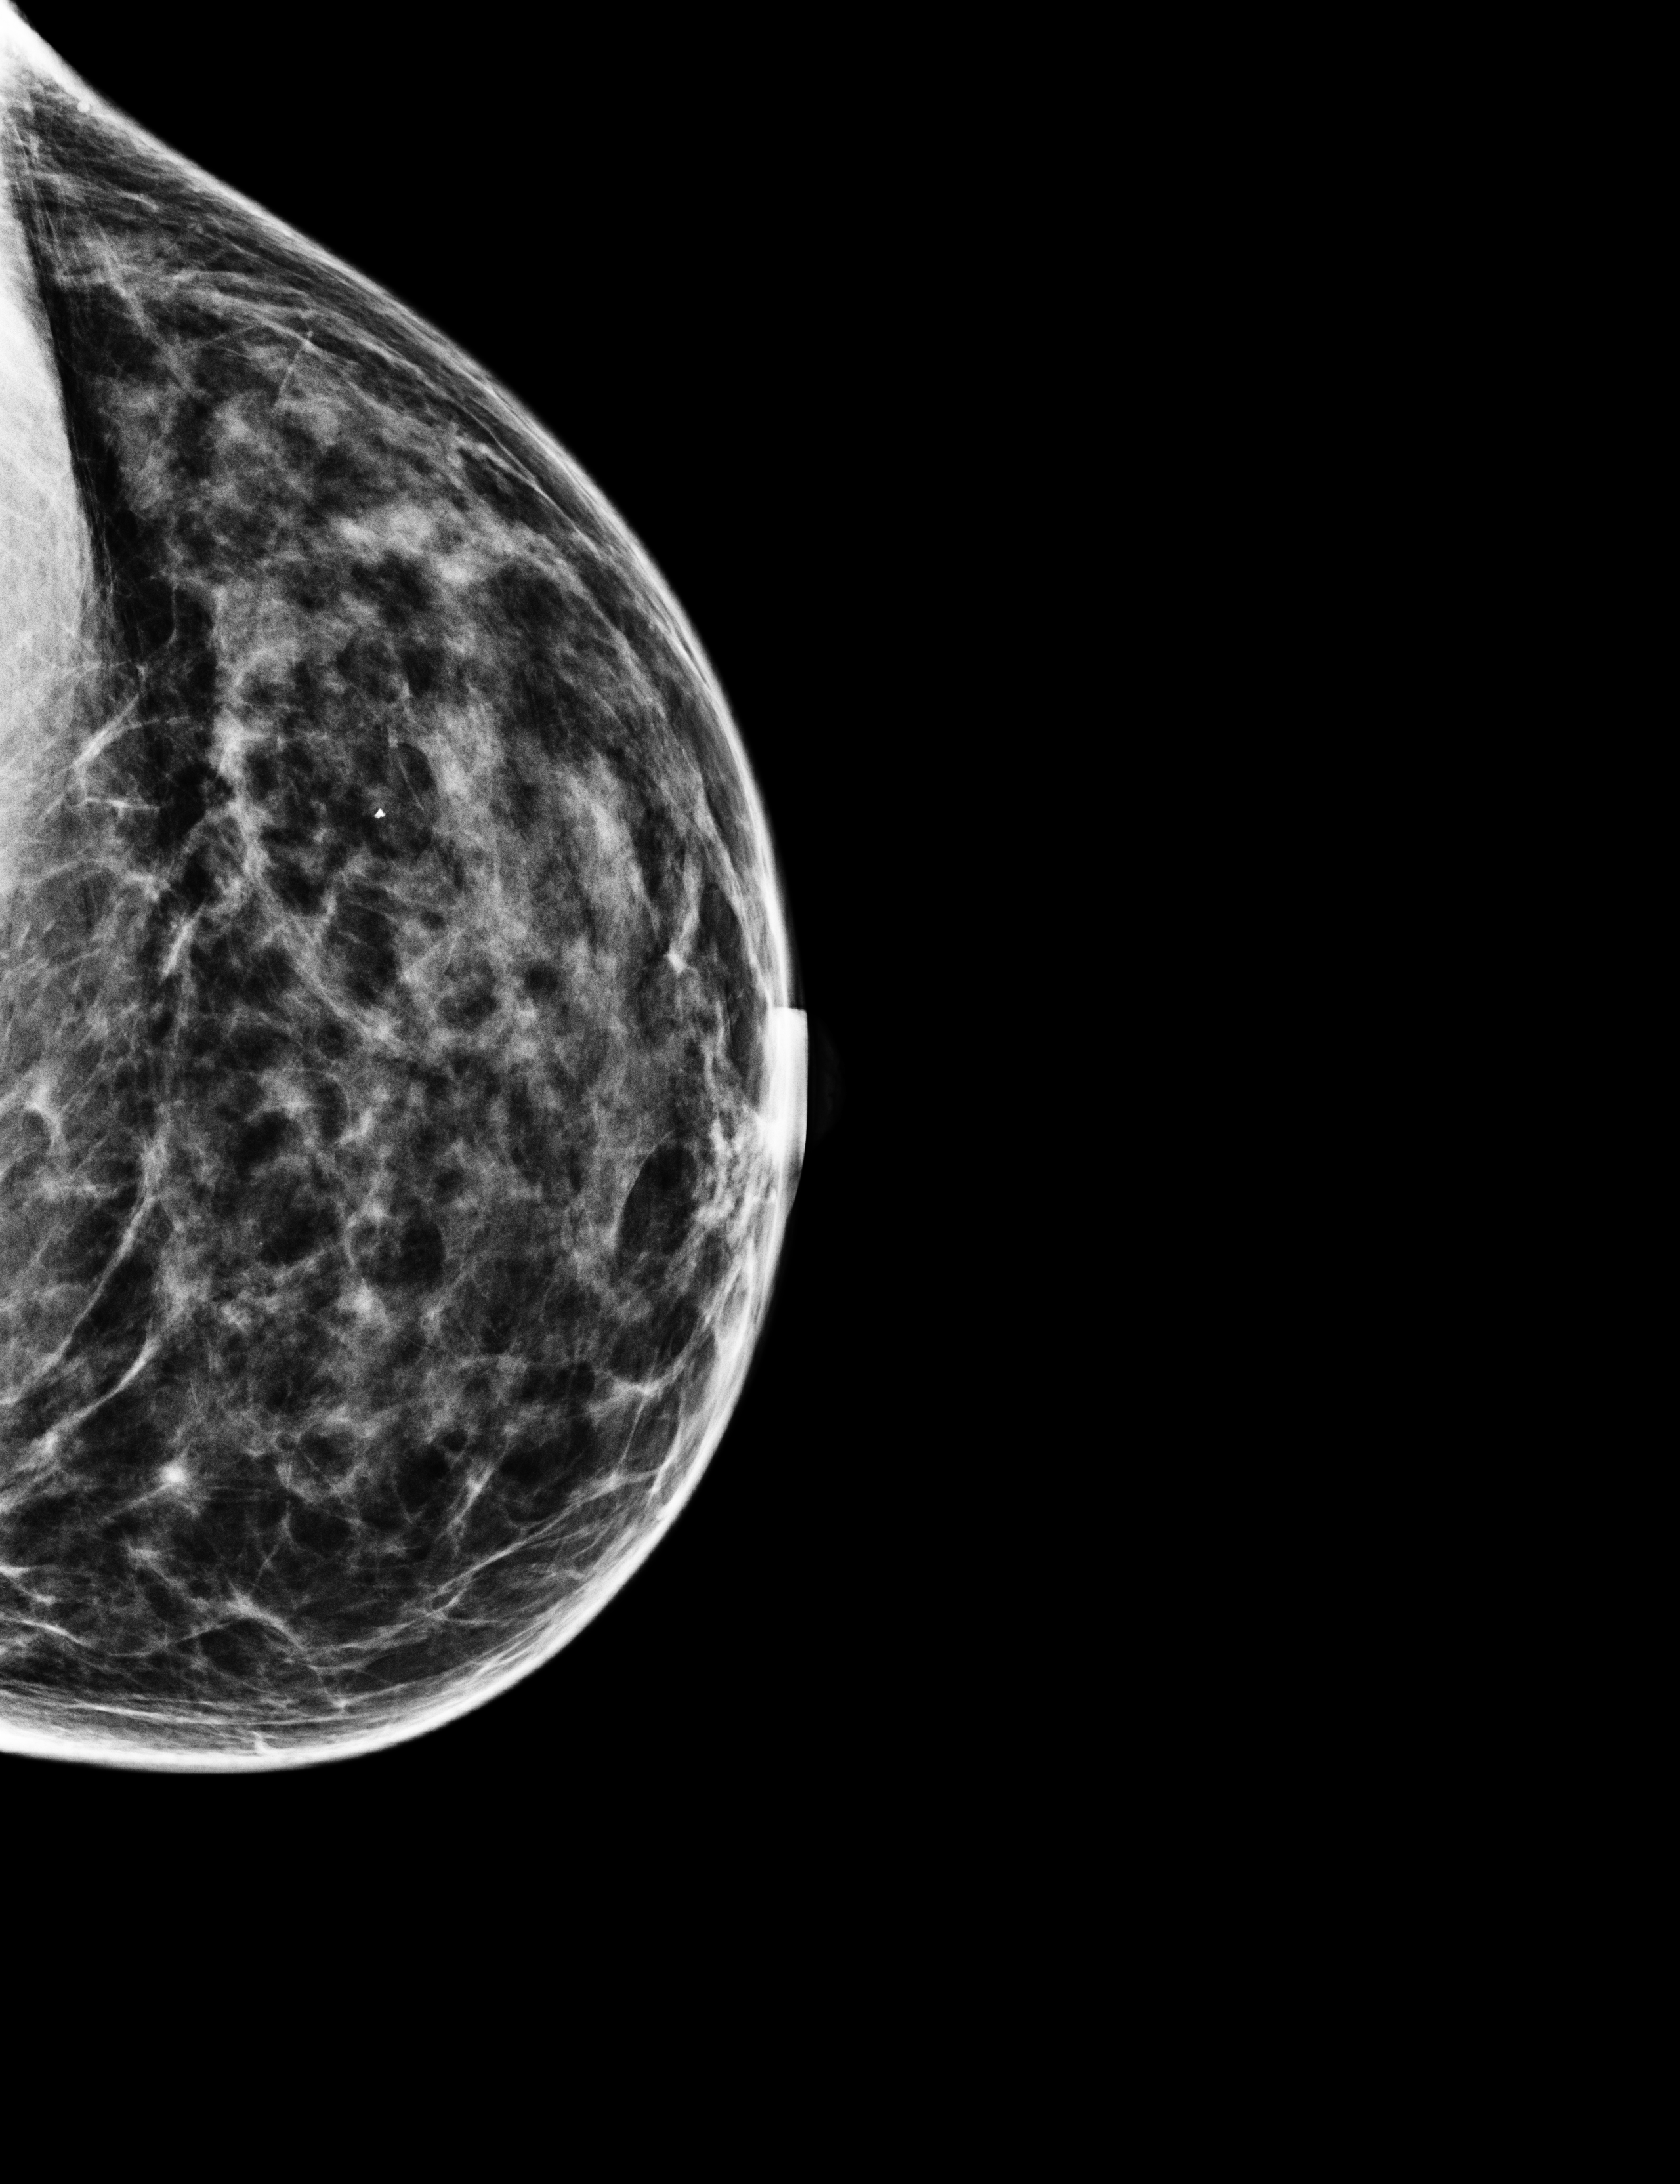
Full-field digital mammogram (FFDM), left breast, CC view, annual screening mammography examination, compressed breast thickness 51 mm, system: Selenia Dimensions. Patient aged 43 years (female).
Breast density at the screening exam (both breasts): heterogeneously dense (BI-RADS density category c). Final BI-RADS assessment for this screening round (tomosynthesis exam, both breasts): category 2. Recall: no recall after this screen.